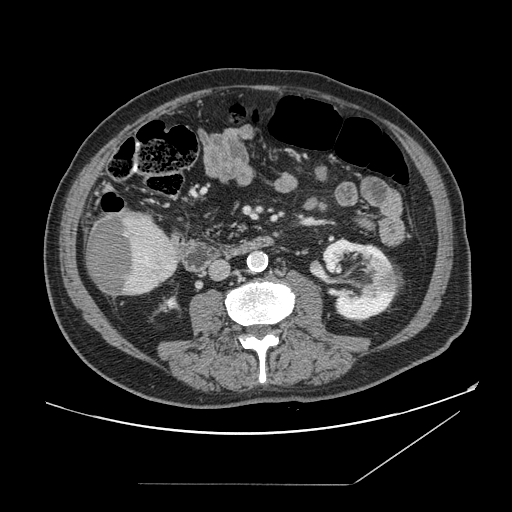
Contrast-enhanced abdominal CT, one axial slice. Position 40 of 166 along the scan axis. 120 kVp. Intravenous contrast given. Soft-tissue window (W 400 / L 40 HU). 512 × 512 image matrix, field of view 416 × 416 mm. Male patient, age 80 years. Case-level facts recorded for this patient, not image findings: diagnosis: colorectal cancer liver metastases, imaged before liver resection; multiple liver metastases: no; largest metastasis: 2.2 cm; chemotherapy before resection: no.
Annotated regions visible in this slice (outlined manually by an expert reader):
- liver: bounding box [x1, y1, x2, y2] px = [87, 210, 178, 296]
- liver metastasis: [90, 215, 134, 292]